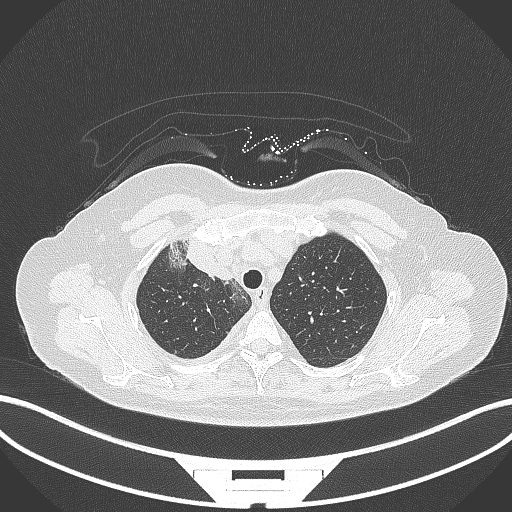
Chest CT, one axial slice; position 251 of 305 along the scan axis; reconstruction kernel B70f; lung window (W 1500 / L -600 HU); 1 mm slice thickness; 512 × 512 image matrix, field of view 400 × 400 mm. Patient: female, 52 years. From the clinical record (not read from this slice): clinical TNM (as recorded): T3 N1 M1.
Outlined on this slice (bounding box drawn by a radiologist):
- lung tumour (recorded histology: adenocarcinoma): bounding box [x1, y1, x2, y2] px = [165, 229, 237, 288]